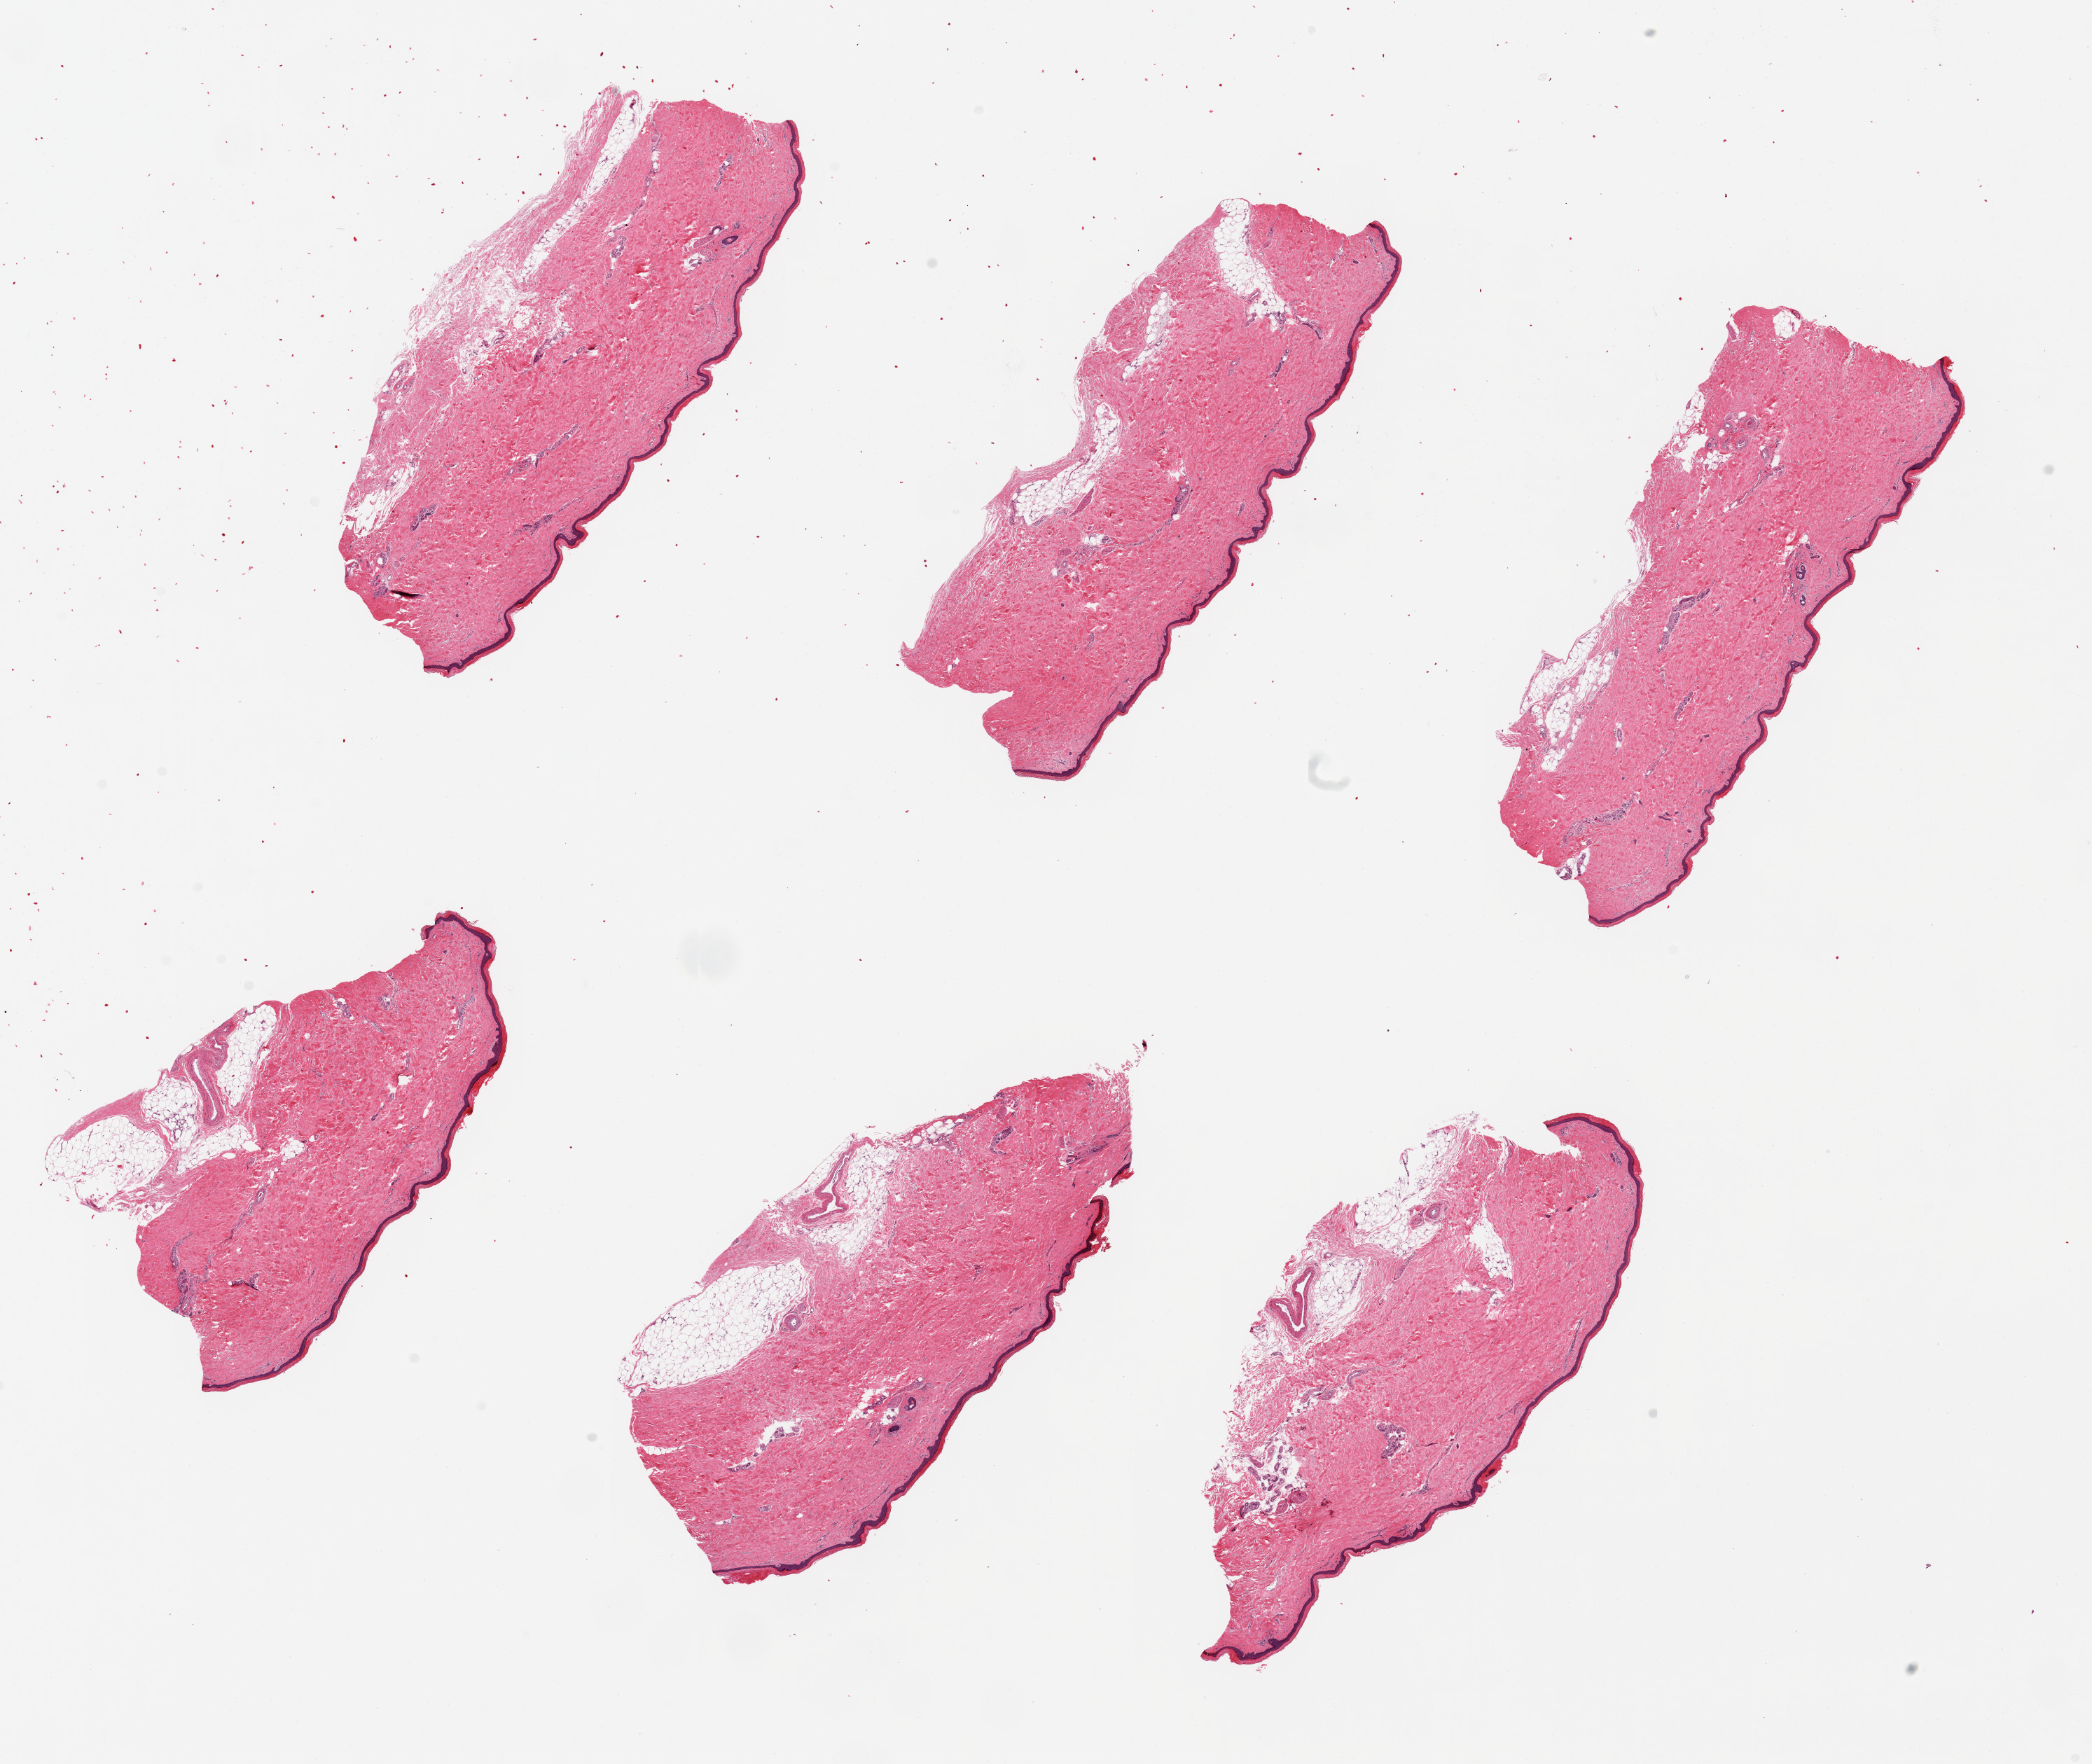
Haematoxylin and eosin whole-slide image — a low-resolution overview of the entire scanned area, about 23.6 x 19.9 mm, PAXgene-fixed, paraffin-embedded tissue, target tissue: skin of lower leg, tissue donor sample. Donor: female.
Pathologist's review note for this sample: 6 pieces. up to 7.5x3mm; up to 1 mm subcutaneous adipose.